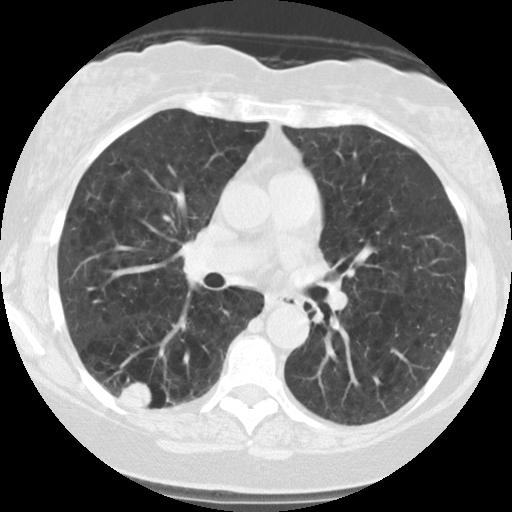
Chest CT (low-dose screening protocol), one axial image; second screening round (one year after baseline); lung window (W 1500 / L -600 HU); 2.5 mm slice thickness; standard (soft-tissue) reconstruction kernel (STANDARD). Female participant, aged 59 years at enrolment. Current smoker at enrolment.
Expert reader's lesion annotation, bounding box (x1, y1, x2, y2) in pixels: (106, 361, 178, 422). The screening reader recorded 2 non-calcified nodules or masses ≥4 mm on this exam; which of them this box marks is not recorded. Participant outcome: lung cancer diagnosed 63 days after this screen — squamous cell carcinoma, NOS, right lower lobe, poorly differentiated (G3), stage IB (AJCC 6th edition), 30 mm at pathology.